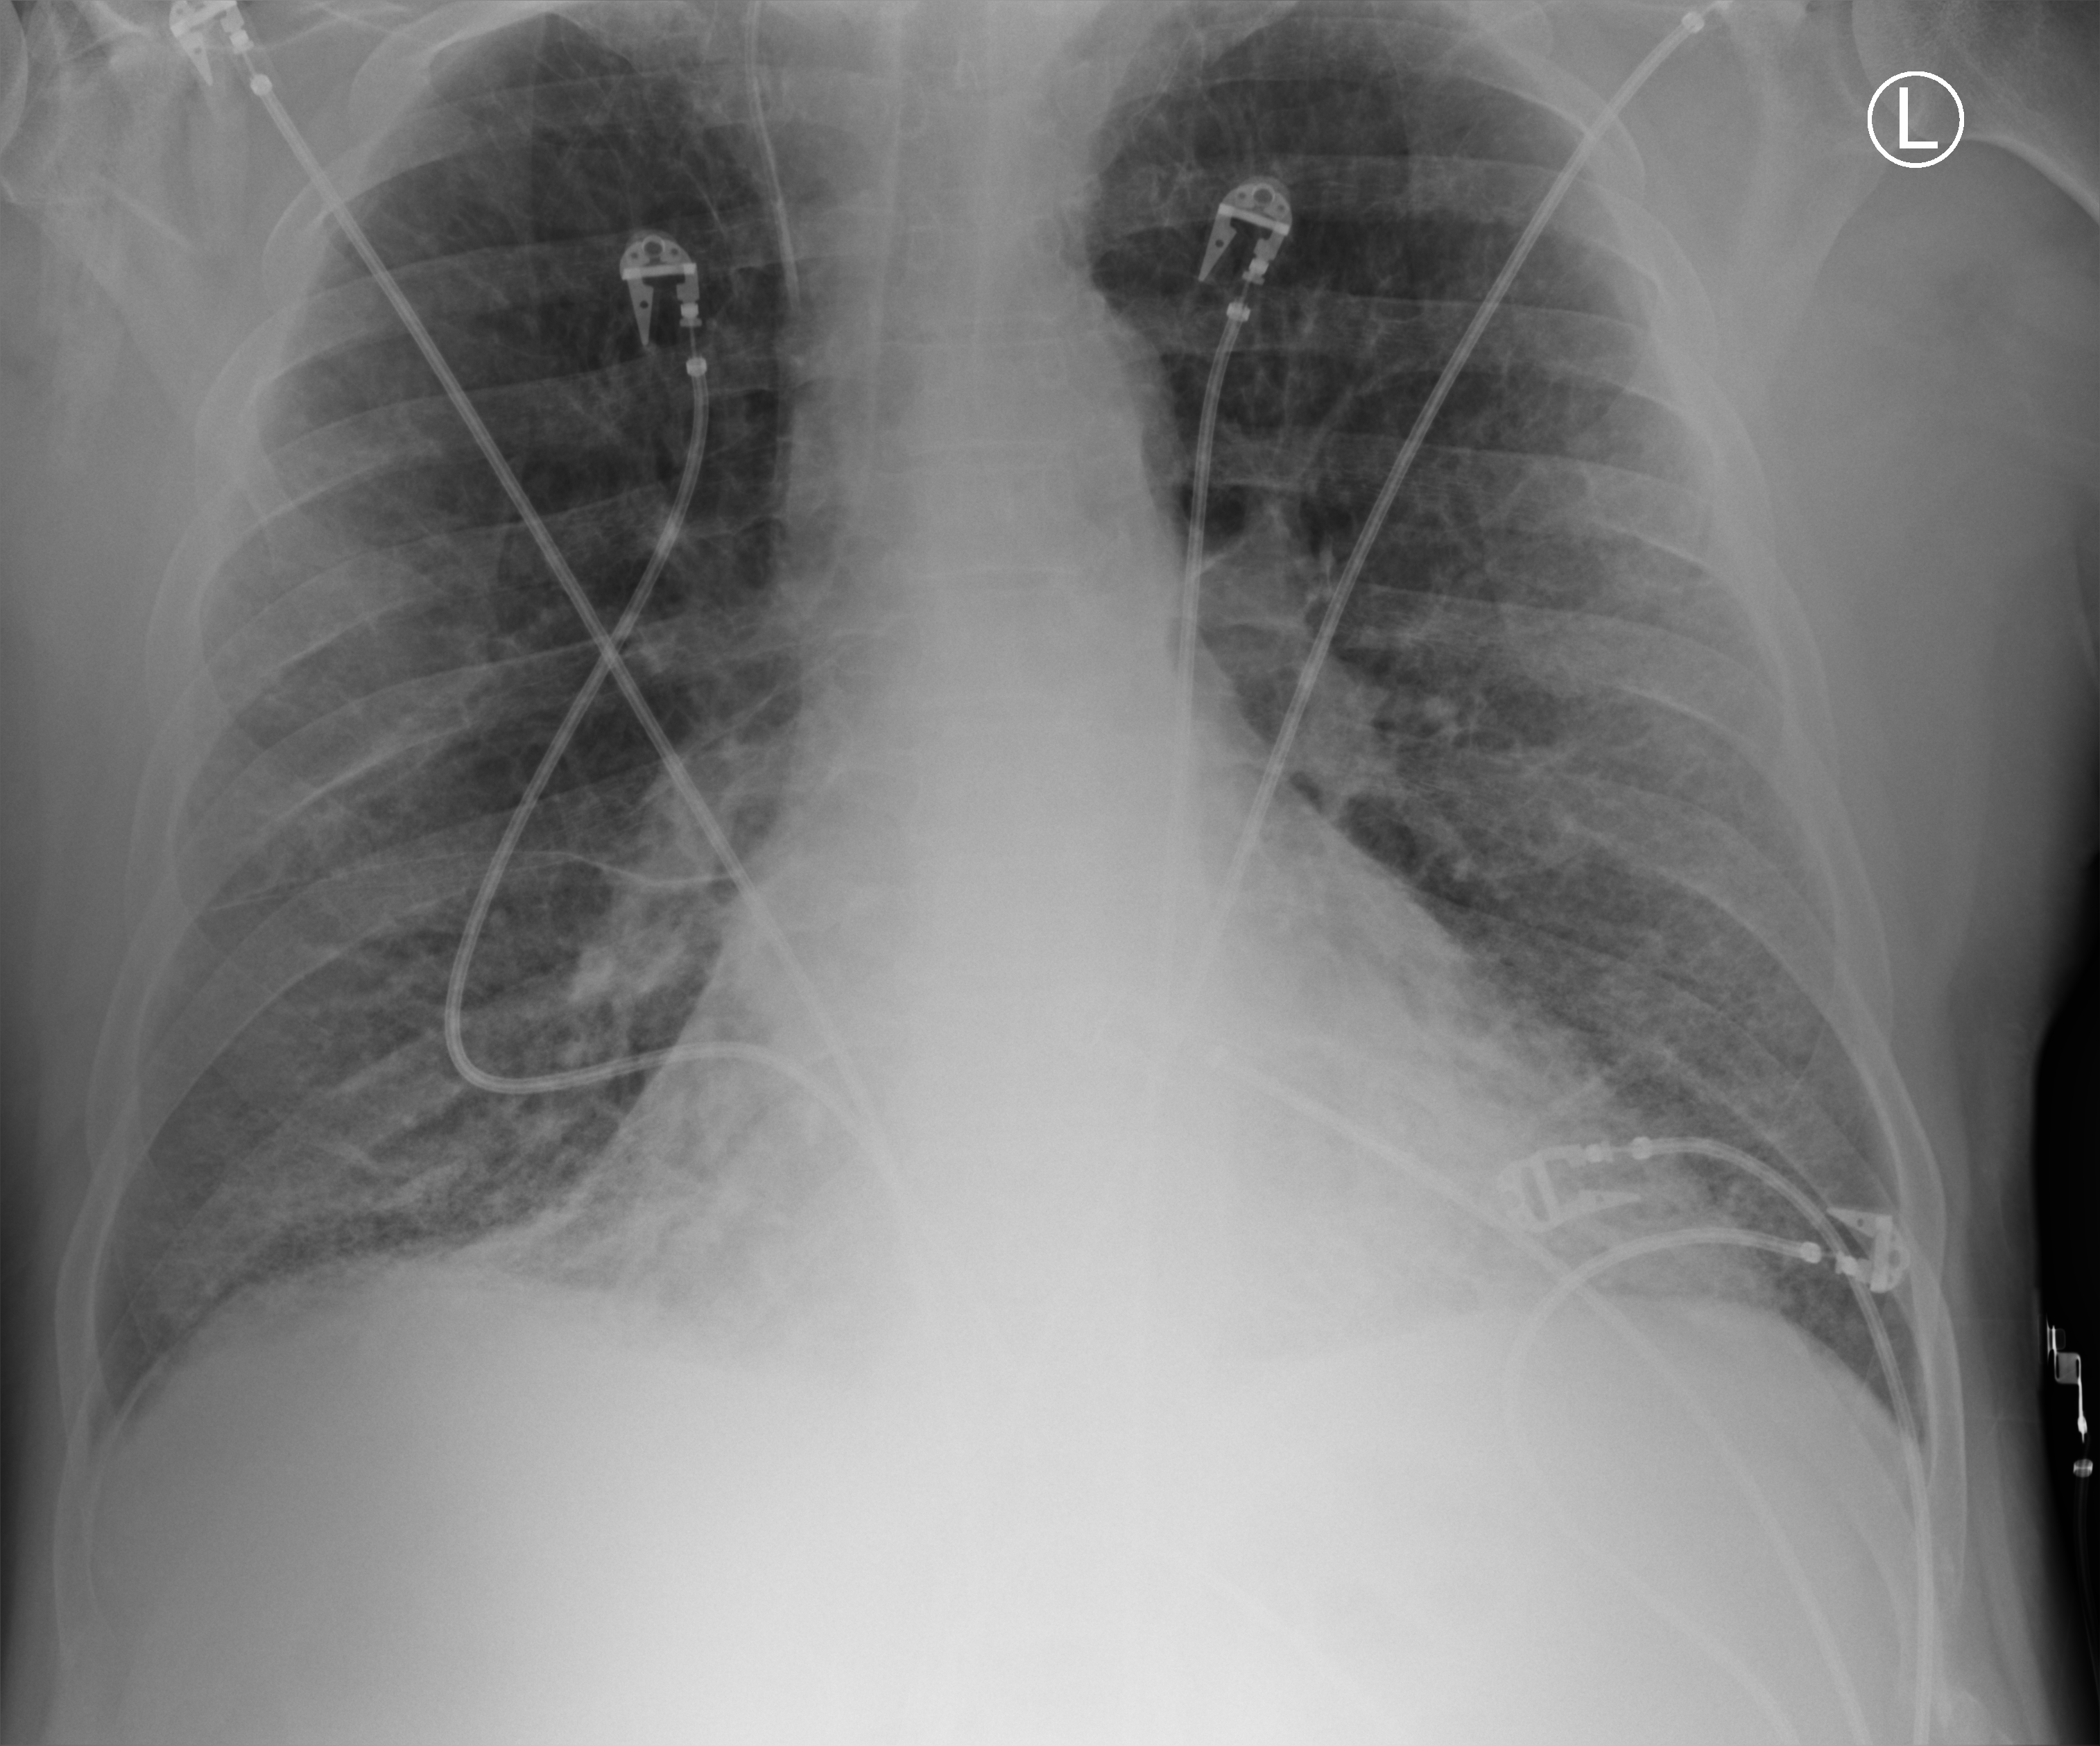
Chest X-ray (portable). Patient hospitalised with COVID-19, aged 18–59 years.
From the hospital-stay record, not from the radiograph (when in the stay this image was taken is not recorded): mechanically ventilated during this hospital stay: no.